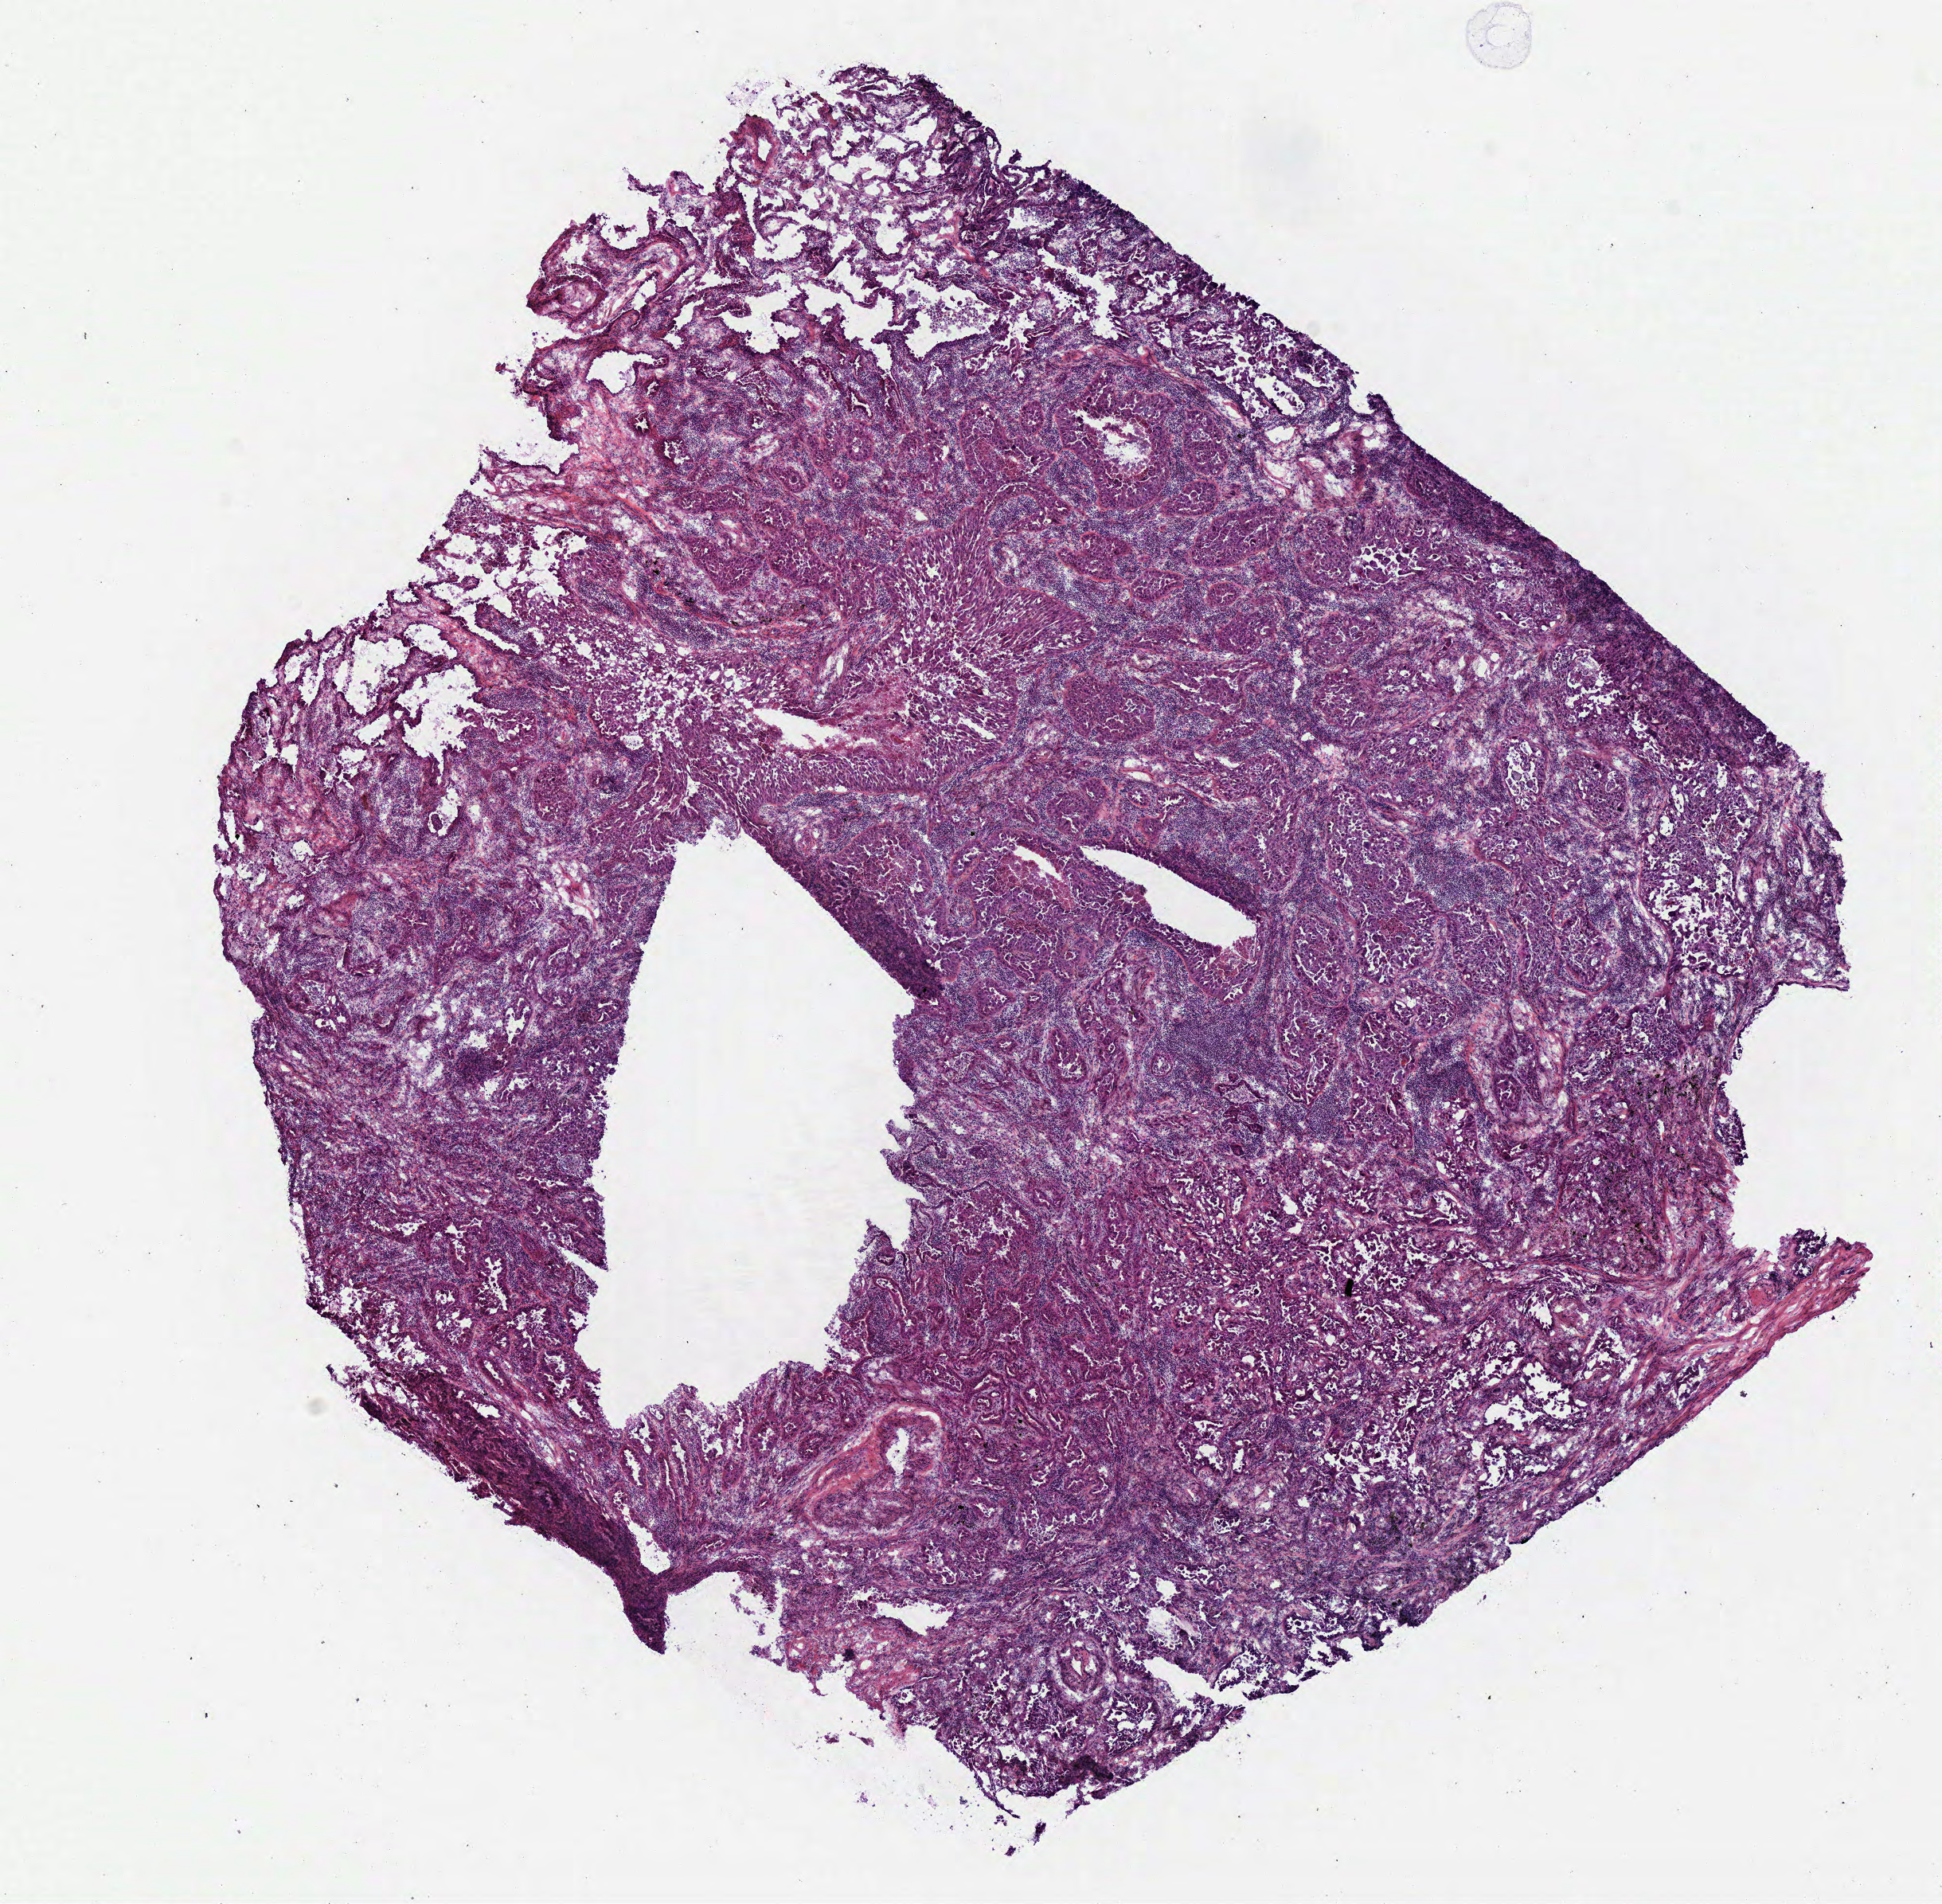
Whole-slide histology image, H&E-stained, a low-resolution overview of the entire scanned area, about 9.6 x 9.4 mm. Frozen section from the bottom of the tissue portion. Lung, primary tumour sample. Patient: male, age at initial diagnosis 71 years.
Pathologic diagnosis: Adenocarcinoma, NOS (upper lobe, lung).